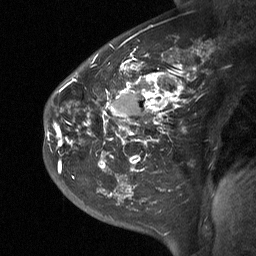
Breast MRI (dynamic contrast-enhanced), one sagittal slice; slice 40 of 64 in the series (ordered by position); dynamic contrast-enhanced study with each time point stored as its own series, time point 2 of 3 at this slice position (early post-contrast, ordered by acquisition time); 1.5 T; TE 4.8 ms, TR 27 ms; 2 mm slice thickness; 256 × 256 image matrix, field of view 200 × 200 mm. Female patient, age 42 years. From the clinical record (not read from this slice): setting: breast cancer imaged before/during neoadjuvant chemotherapy; receptor status: triple-negative.
Annotated regions visible in this slice (semi-automatic segmentation, software-assisted and operator-edited):
- analysis volume of interest (the breast-tissue region the enhancement analysis was run in; not a lesion): bounding box [x1, y1, x2, y2] px = [44, 29, 203, 190]
- tumour enhancement mask (voxels above the 90 % enhancement threshold inside the analysis volume of interest): [47, 64, 194, 173]